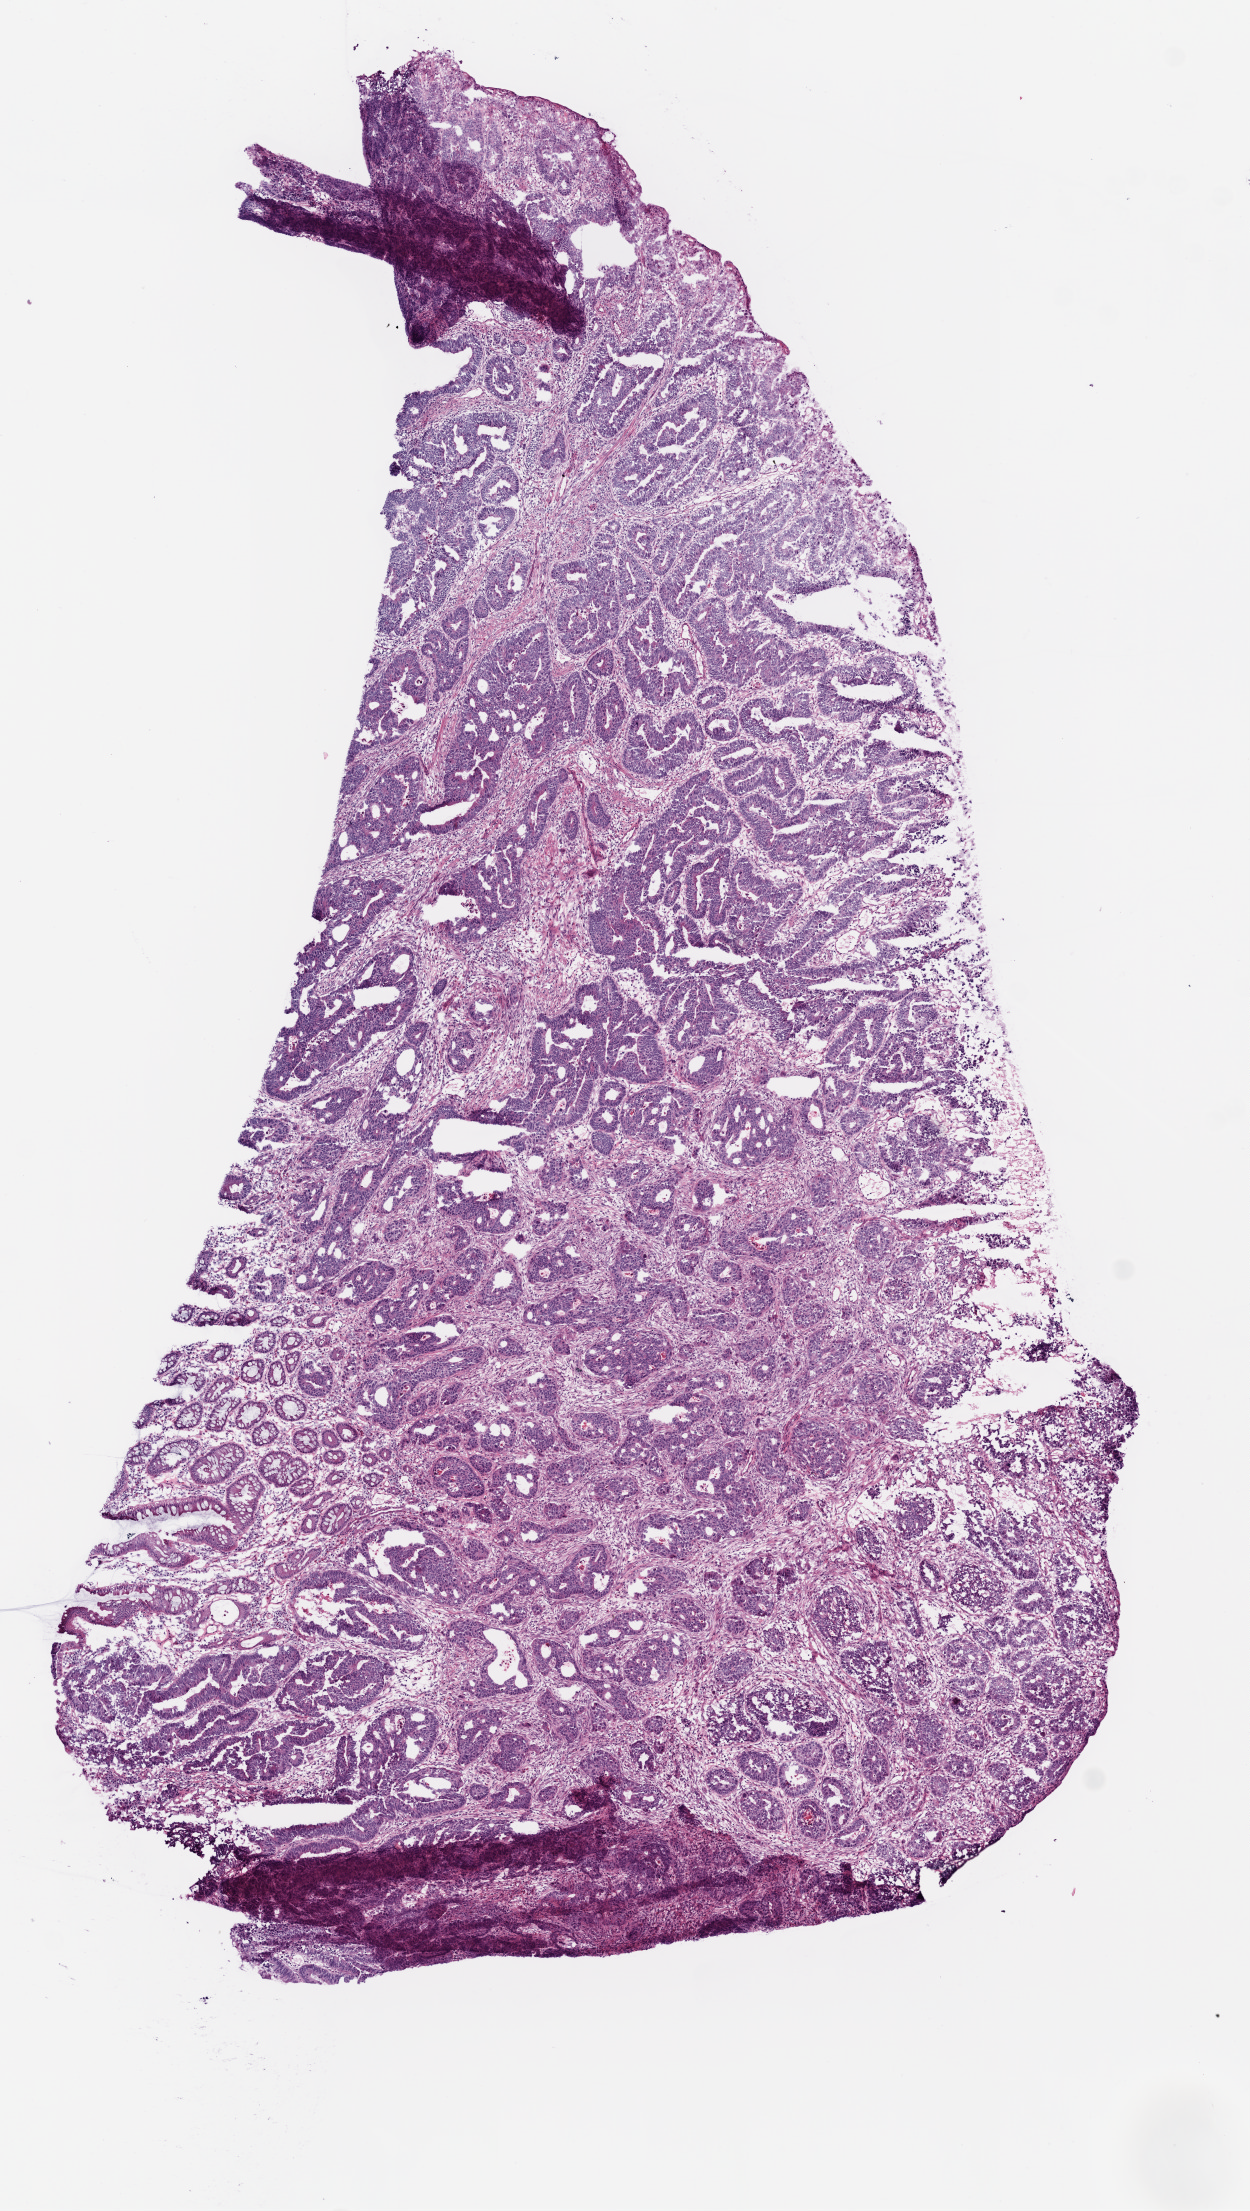
Whole-slide histology image, H&E-stained — shown as a low-resolution overview of the whole scanned area (about 5.0 x 8.9 mm, slide scanned at 20x), frozen section, primary tumour sample from the colon. Patient: male, age at initial diagnosis 82 years. Composition of this section per pathologist review: tumour cells 70%, tumour nuclei 80%, normal cells 5%, stromal cells 25%, necrosis 0%.
Histologic diagnosis: Adenocarcinoma, NOS. AJCC pathologic stage: IIIC. TNM: T3 N2 M0. Lymph nodes positive (case pathology): 7 of 28 examined.